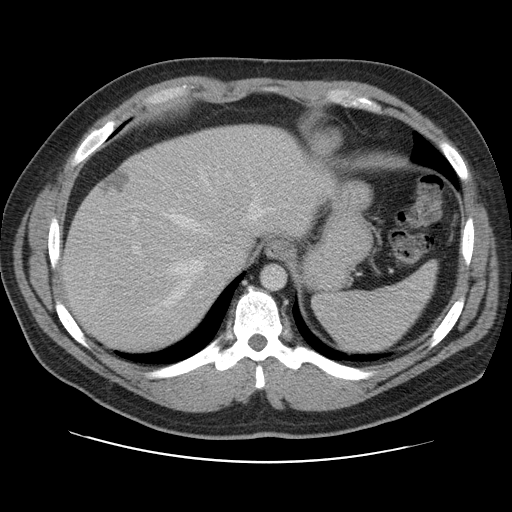
Contrast-enhanced abdominal CT, one axial slice; position 88 of 109 along the scan axis; intravenous contrast given; soft-tissue window (W 400 / L 40 HU); 512 × 512 image matrix, field of view 402 × 402 mm. Male patient, age 35 years. Case-level facts recorded for this patient, not image findings: diagnosis: colorectal cancer liver metastases, imaged before liver resection; multiple liver metastases: yes; largest metastasis: 2.8 cm; disease in both lobes: yes.
Outlined on this slice (outlined manually by an expert reader):
- hepatic veins: bounding box [x1, y1, x2, y2] px = [141, 170, 271, 317]
- liver: [63, 125, 326, 353]
- planned liver remnant (the part of the liver to remain after resection): [63, 125, 327, 353]
- portal vein (with intrahepatic branches): [128, 162, 210, 278]
- liver metastasis: [102, 171, 130, 194]